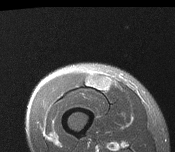
MRI of an extremity soft-tissue mass, one axial slice. Slice 36 of 116 in the series (ordered by position). T2-weighted fat-saturated. MR volume resampled by the dataset authors to the PET/CT grid (not the native acquisition matrix). 3.27 mm slice thickness. 175 × 152 image matrix. Male patient. From the clinical record (not read from this slice): histological type: pleiomorphic leiomyosarcoma; grade: intermediate; site of the primary tumour: right thigh.
Structures marked on this image (expert contour drawn on MRI and transferred to this co-registered scan by the dataset authors):
- gross tumour volume including surrounding oedema: bounding box (x1, y1, x2, y2) in pixels: (85, 74, 110, 91)